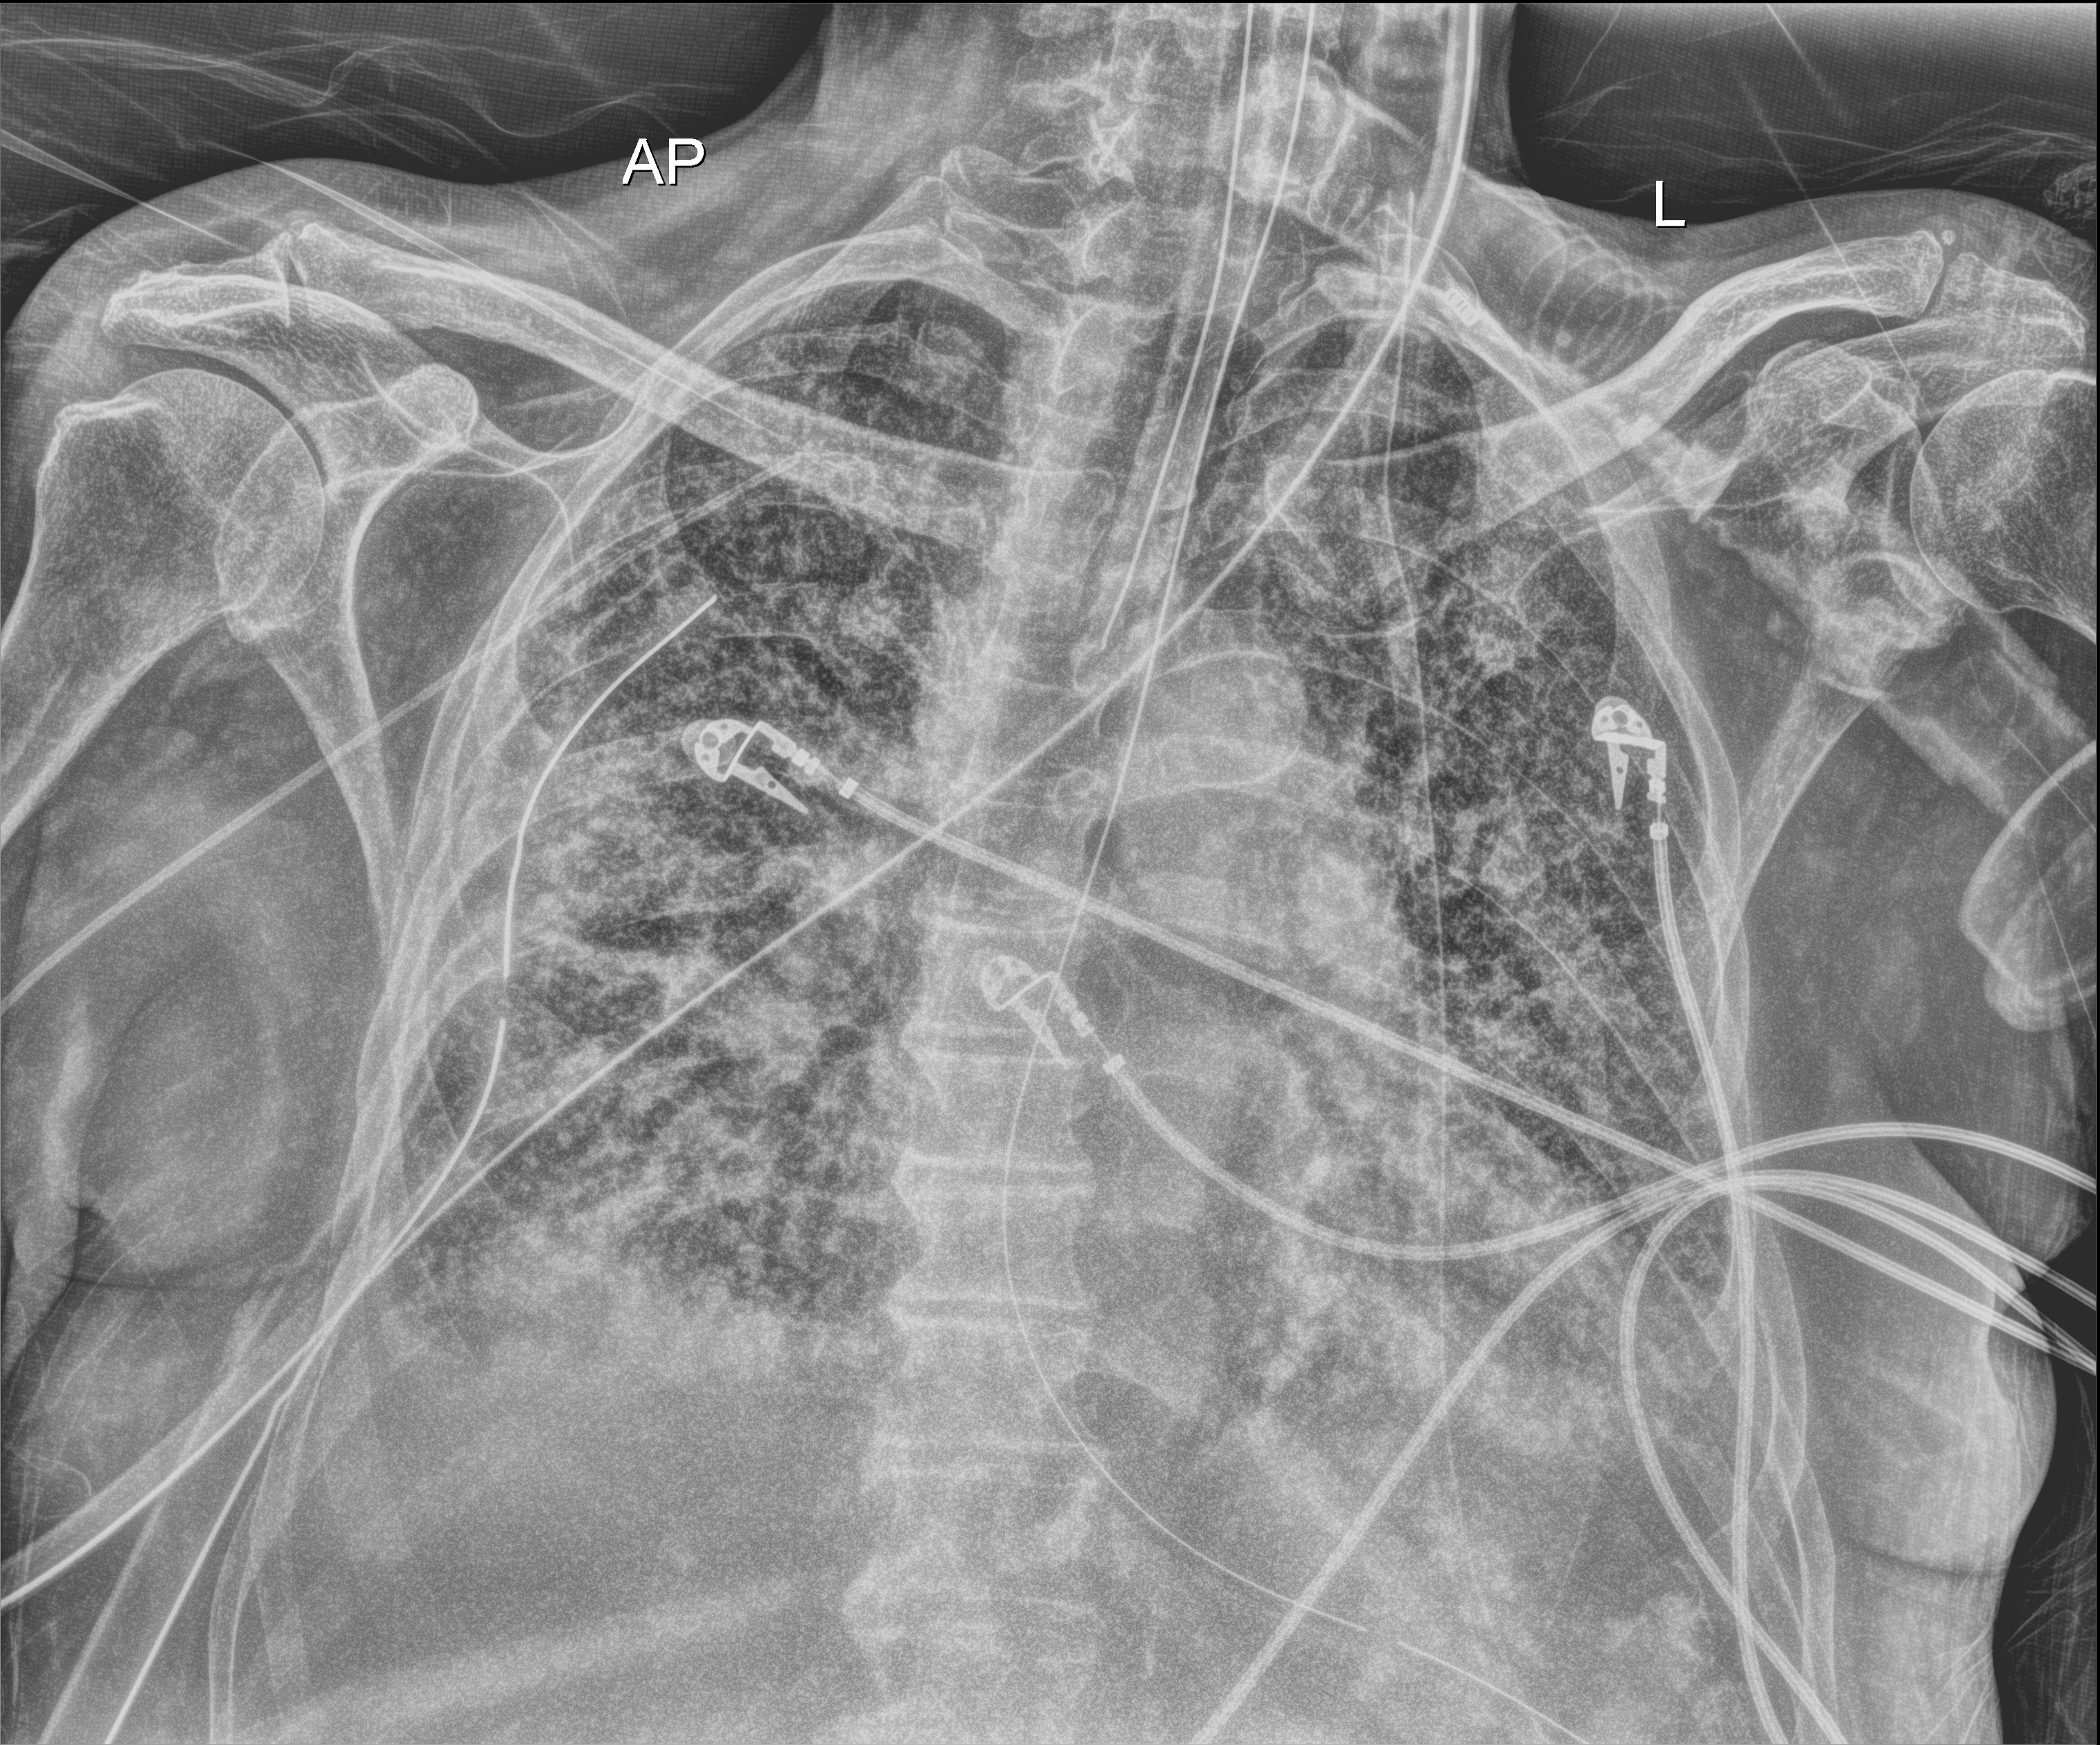
Bedside chest radiograph (digital radiography); anteroposterior (AP) projection. Male patient hospitalised with COVID-19, age 75–90 years.
Admission-level facts for this patient (not findings on this image; timing relative to this image not recorded): mechanically ventilated during this hospital stay: yes; admitted to intensive care during this hospital stay: yes; chronic kidney disease (admission record): no.